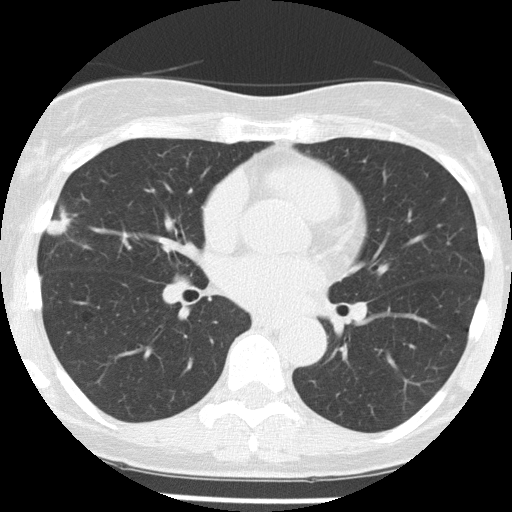
Low-dose screening chest CT, one axial slice. Slice 82 of 156 in the series (ordered by position). Reconstruction kernel FC51. 120 kVp. Lung window (W 1500 / L -600 HU). 2 mm slice thickness. 512 × 512 image matrix, field of view 280 × 280 mm.
Annotated regions visible in this slice (manually delineated by an expert):
- lesion 1 (tumor, middle lobe of right lung): box from (x=47, y=208) to (x=77, y=241) px